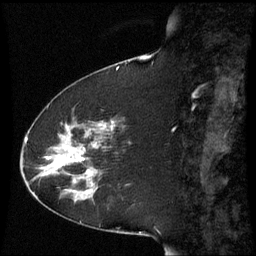
Breast MRI (dynamic contrast-enhanced), one sagittal slice. Slice 18 of 60 in the series (ordered by position). Dynamic contrast-enhanced series, image 2 of 3 at this slice position (ordered by acquisition). 1.5 T. TE 4.2 ms, TR 8.9 ms. 256 × 256 image matrix. Patient: female, 51 years. From the clinical record (not read from this slice): setting: breast cancer imaged before/during neoadjuvant chemotherapy; receptor status: HR-positive, HER2-negative.
Structures marked on this image (semi-automatically segmented with operator editing):
- analysis volume of interest (the breast-tissue region the enhancement analysis was run in; not a lesion): box from (x=50, y=121) to (x=117, y=187) px
- tumour enhancement mask (voxels above the 70 % enhancement threshold inside the analysis volume of interest): (x=50, y=128)–(x=90, y=175)